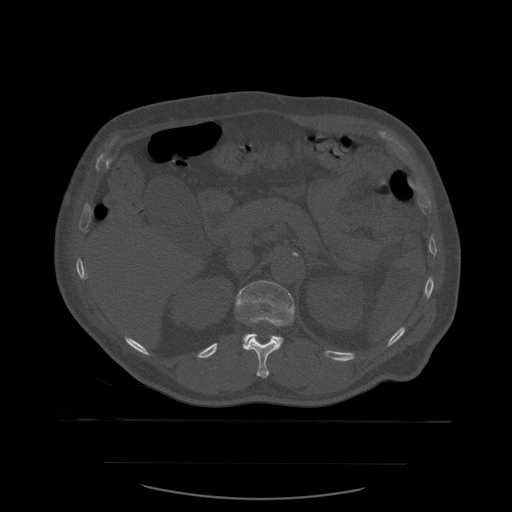
CT including the spine, one axial slice; slice 261 of 590 in the series (ordered by position); bone window (W 1800 / L 400 HU); 1.25 mm slice thickness; 512 × 512 image matrix, field of view 479 × 479 mm. Patient age 71 years. From the clinical record (not read from this slice): primary cancer: lung; vertebrae with lytic lesions (as recorded): T1, T2, L5, S1.
Structures marked on this image (semi-automatic segmentation, software-assisted and operator-edited):
- L1 vertebra: bounding box <236,281,295,344> (left, top, right, bottom; pixels)
- T12 vertebra: <242,319,282,379>